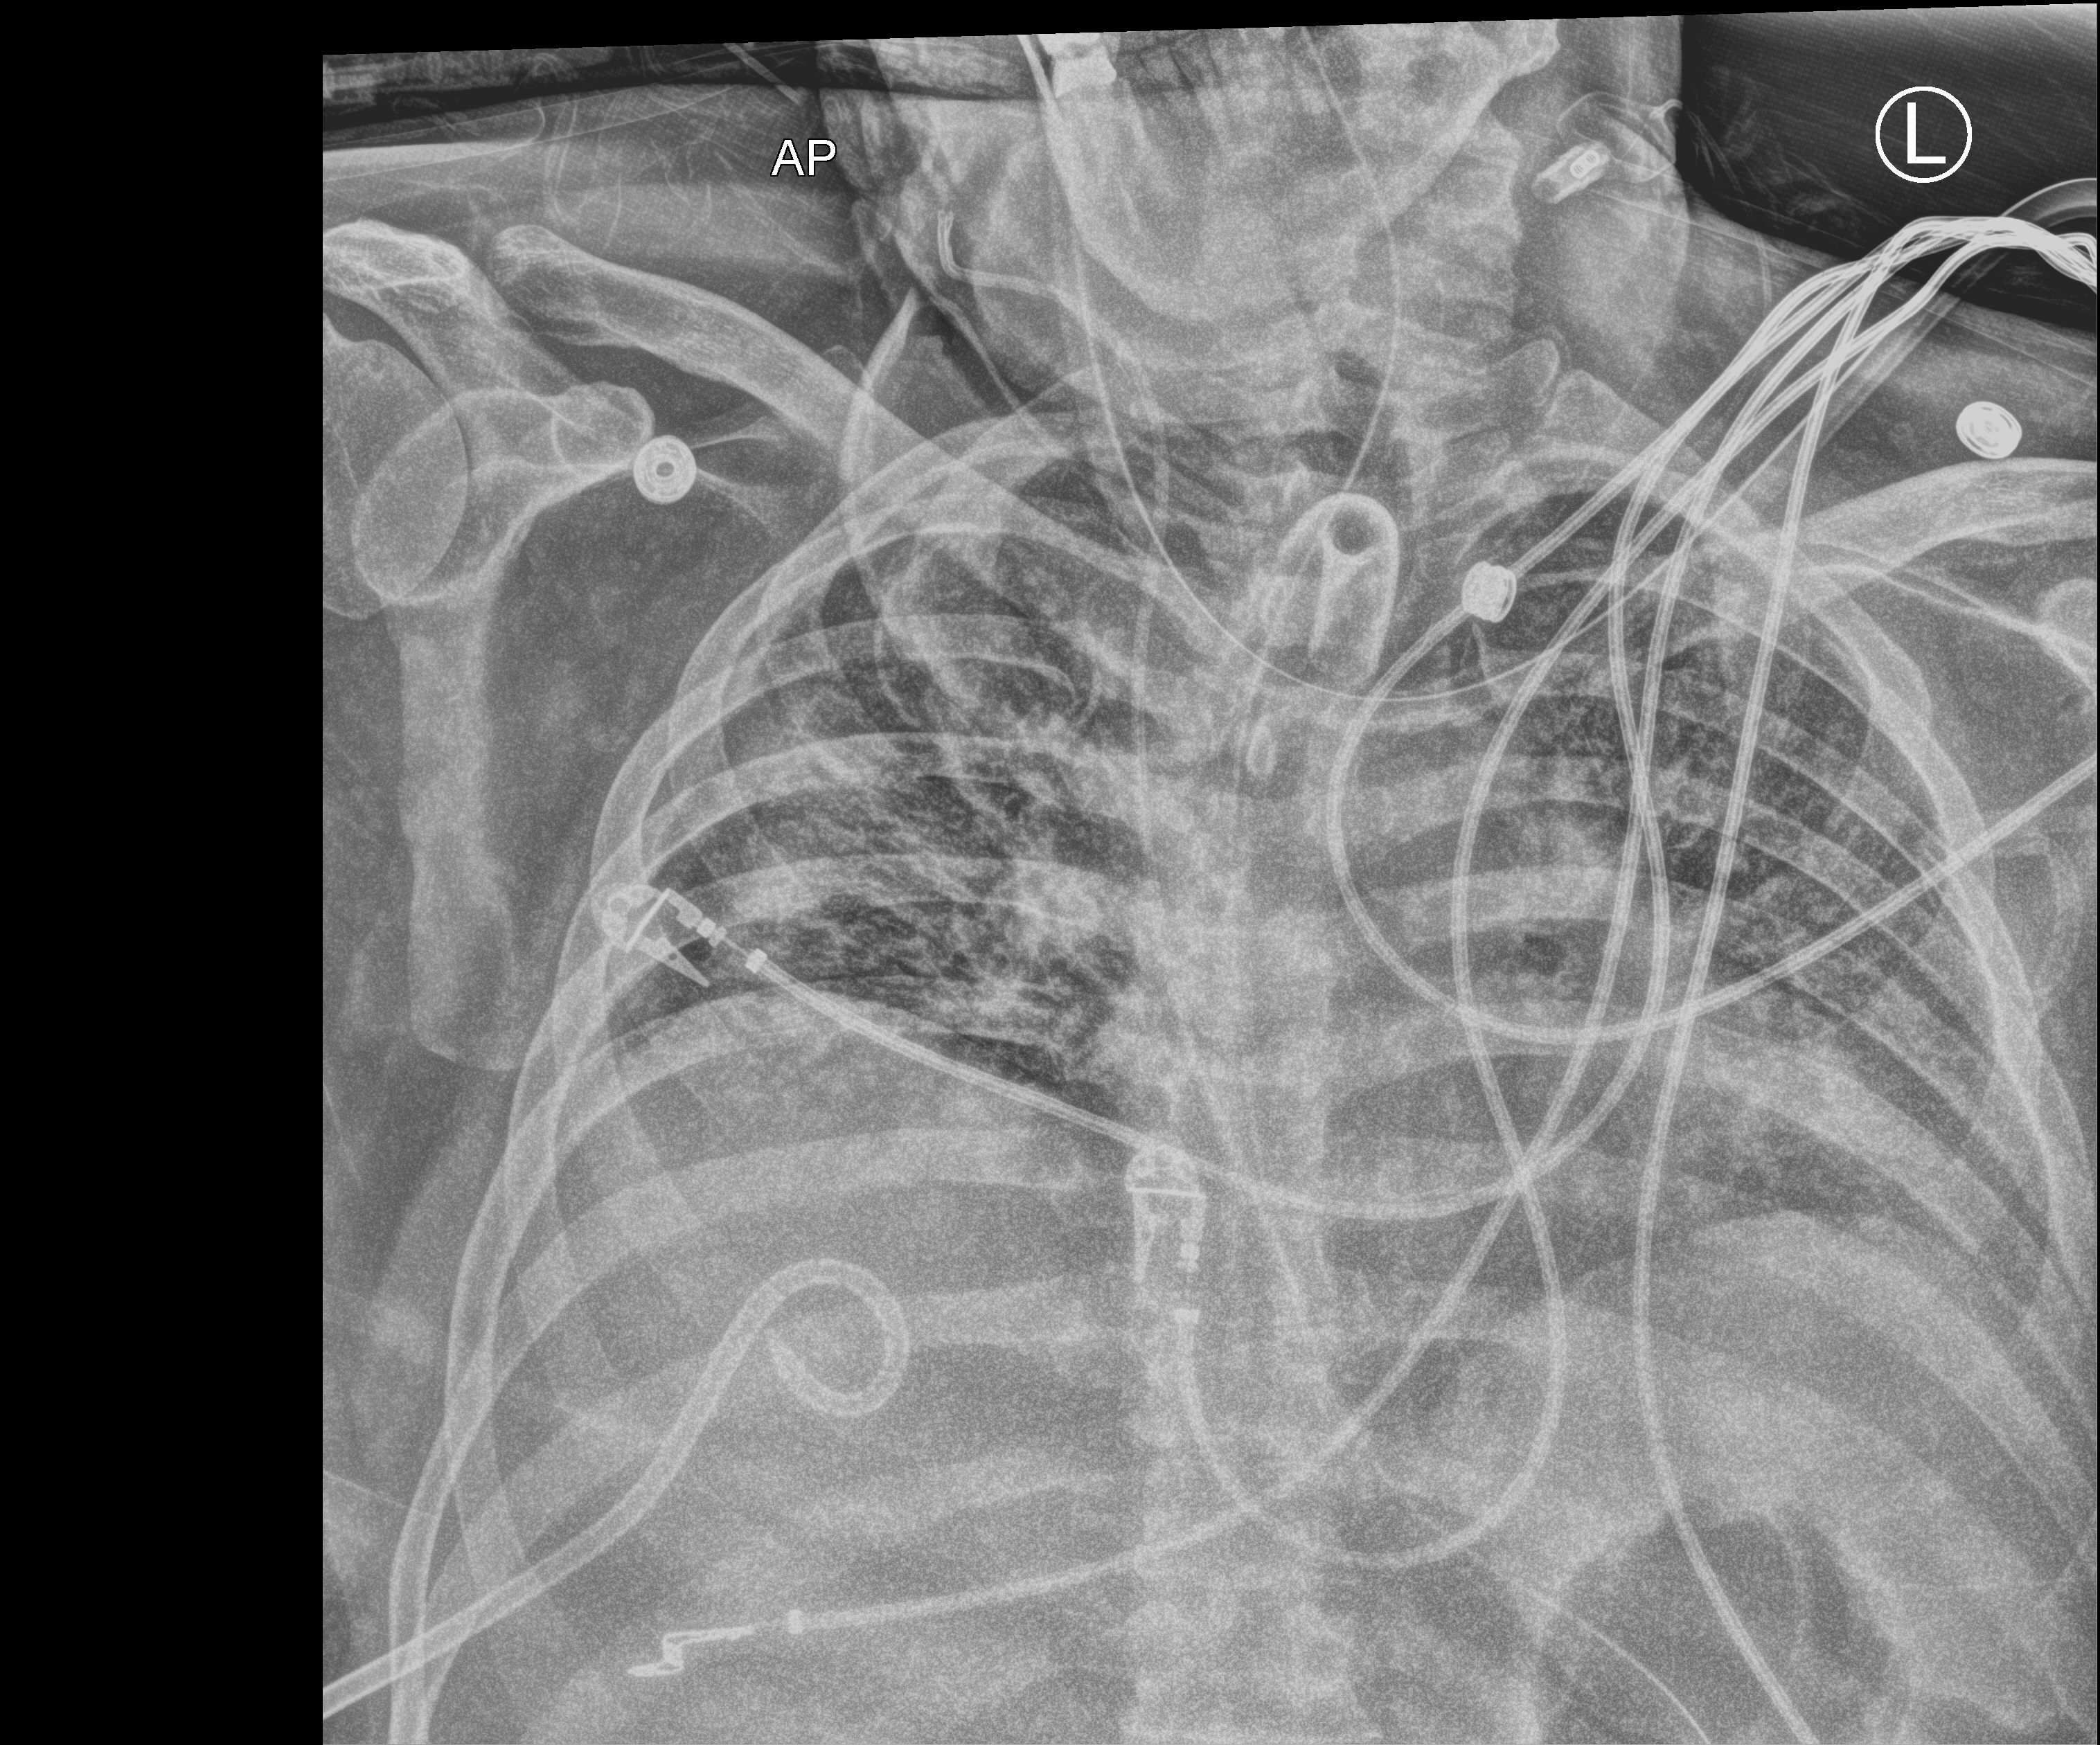
Portable chest radiograph, anteroposterior (AP) projection. Patient hospitalised with COVID-19; male, aged 18–59 years.
From the hospital-stay record, not from the radiograph (when in the stay this image was taken is not recorded): COPD (admission record): no; admitted to intensive care during this hospital stay: yes.